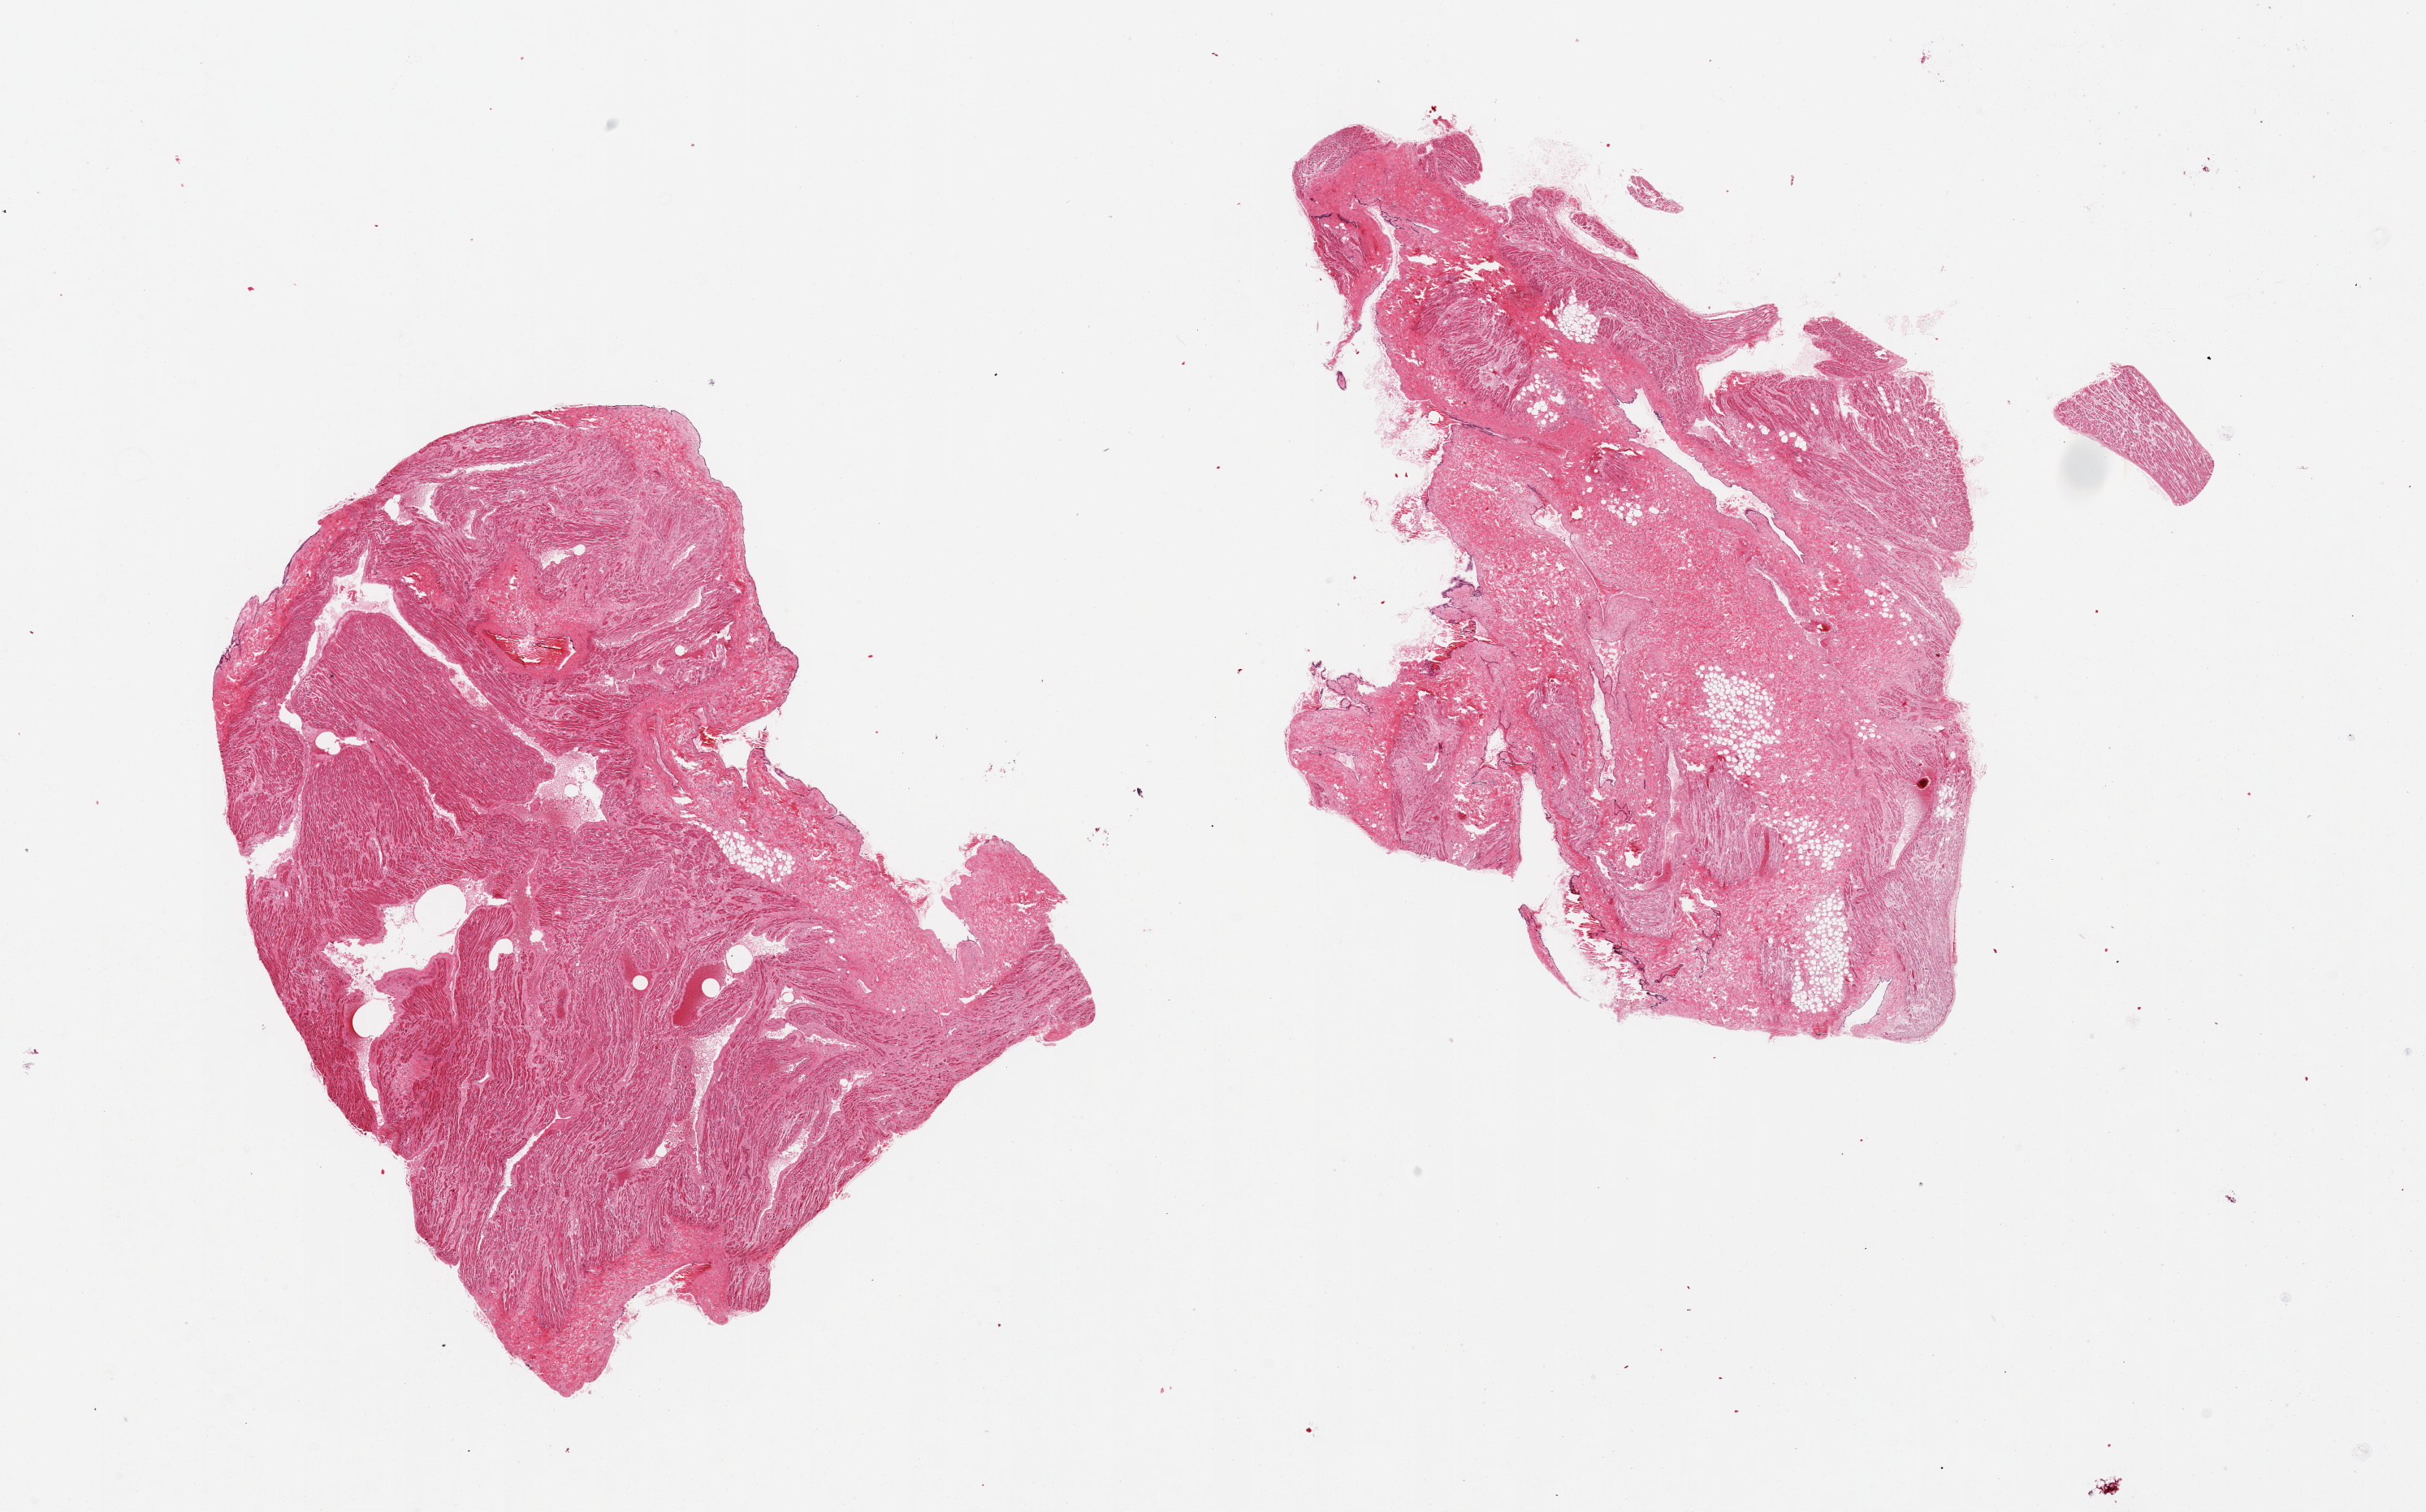
Digitized H&E-stained section, brightfield — shown as a low-resolution overview of the whole scanned area (about 23.6 x 14.7 mm), PAXgene-fixed, paraffin-embedded tissue, sampled site (target tissue): auricular appendage, tissue donor sample.
Reviewer comment on this tissue sample: 2 pieces; 1 has large central fibroadipose collection, 50% of piece.